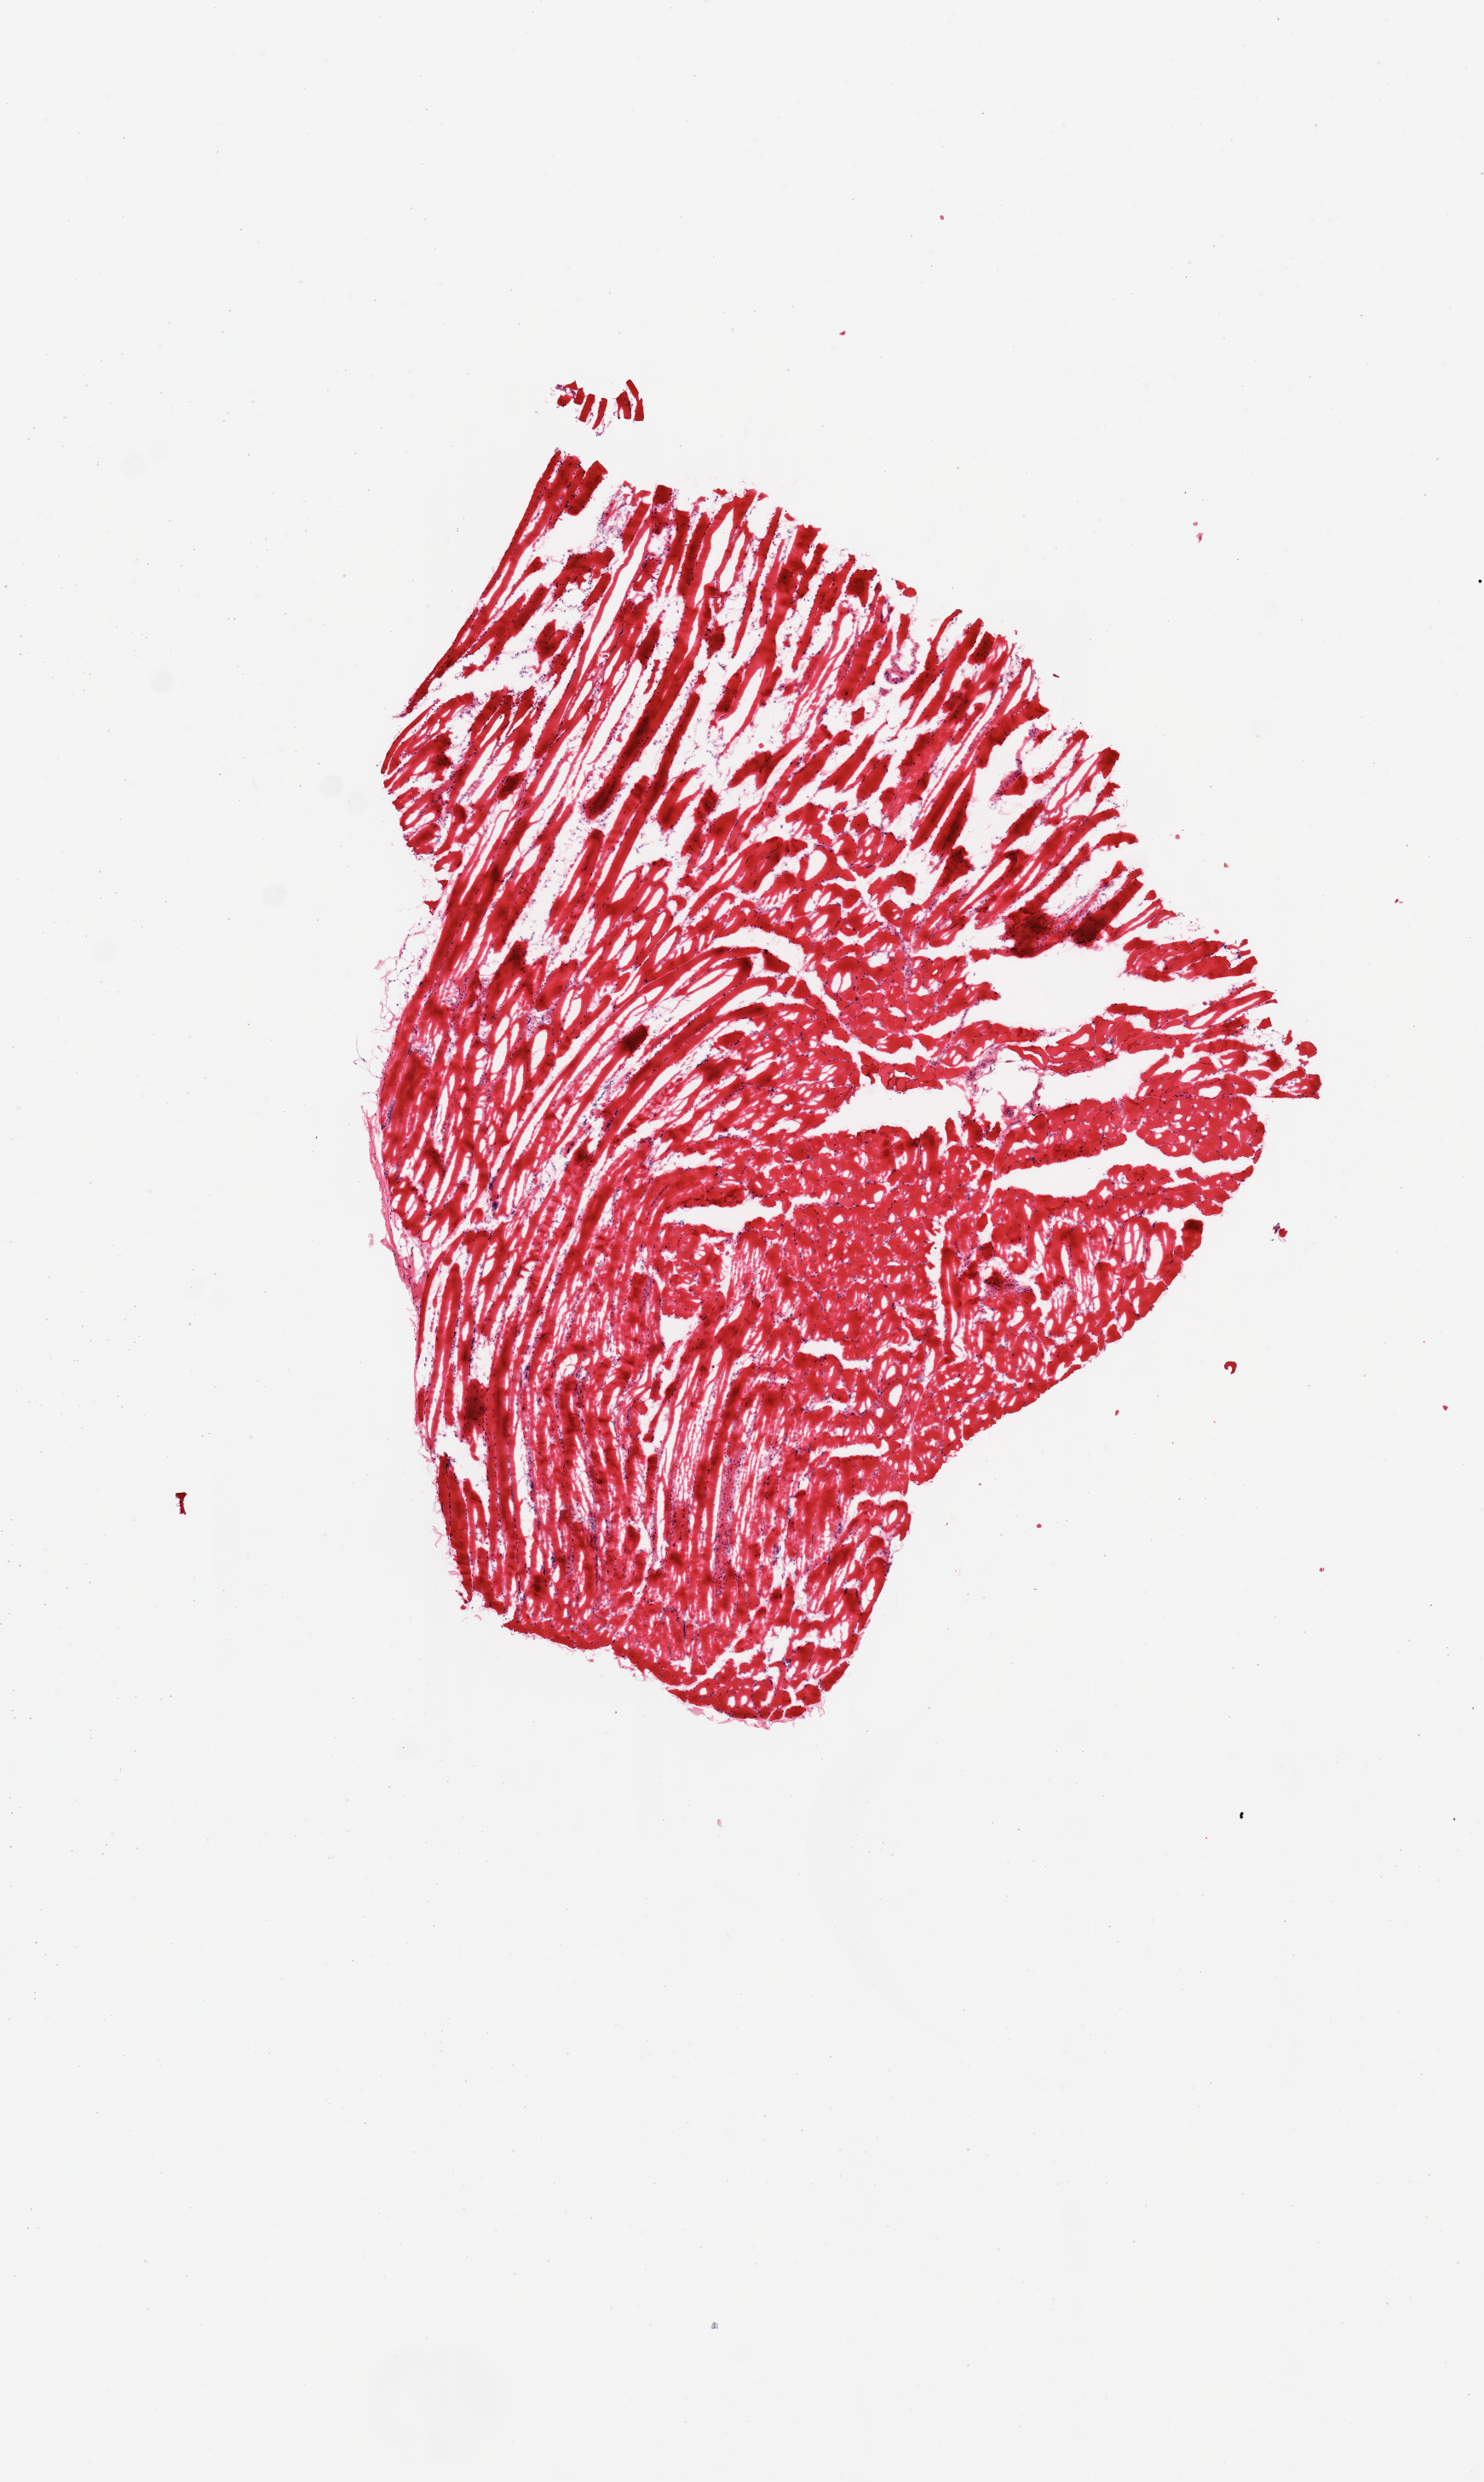
Haematoxylin and eosin whole-slide image — shown as a low-resolution overview of the whole scanned area (about 6.9 x 11.5 mm). Donor sex: female.
Specimen: frozen section (dry ice); section of skeletal muscle (target tissue); donor tissue sample.